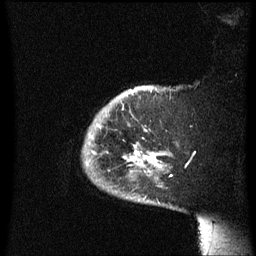
Breast MRI (dynamic contrast-enhanced), one sagittal slice; slice 52 of 60 in the series (ordered by position); dynamic contrast-enhanced series, image 2 of 3 at this slice position (ordered by acquisition); 1.5 T; TE 4.2 ms, TR 8.4 ms; 256 × 256 image matrix. Patient: female, 38 years. From the clinical record (not read from this slice): setting: breast cancer imaged before/during neoadjuvant chemotherapy; receptor status: HER2-positive.
Outlined on this slice (semi-automatically segmented with operator editing):
- analysis volume of interest (the breast-tissue region the enhancement analysis was run in; not a lesion): bounding box (x1, y1, x2, y2) in pixels: (82, 86, 180, 209)
- tumour enhancement mask (voxels above the 70 % enhancement threshold inside the analysis volume of interest): (91, 136, 161, 167)